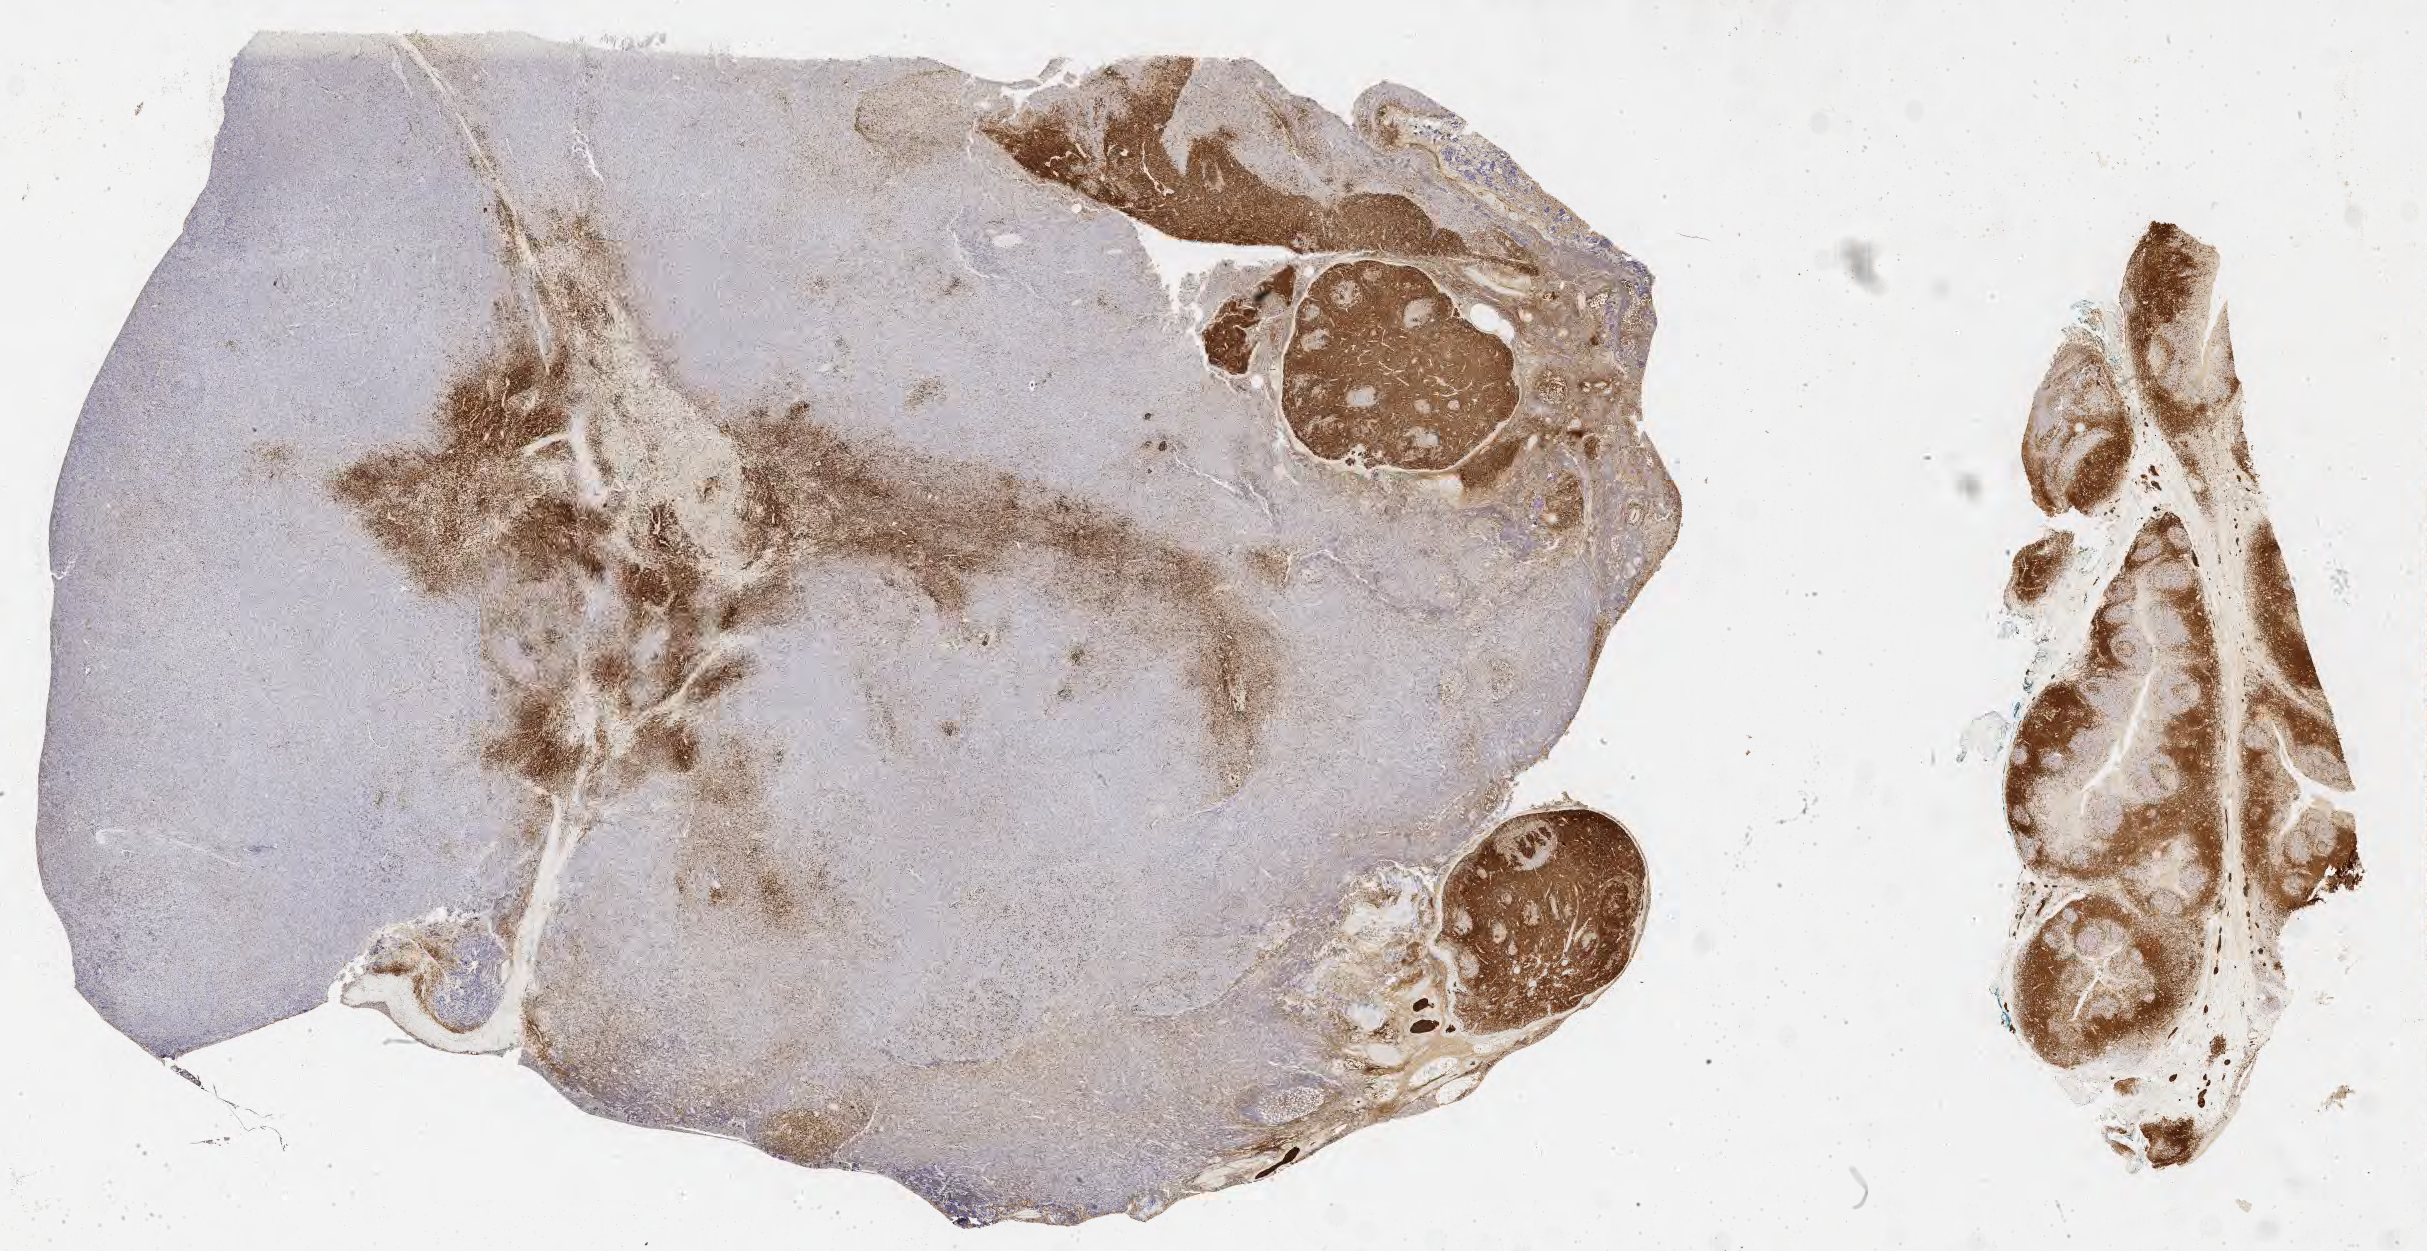
Whole-slide image, immunohistochemical stain for CD3 — low-resolution overview of the scanned area, about 39.2 x 20.2 mm, specimen: tumor tissue, site: lymph node of head and neck. Male, age 3 years at initial diagnosis.
- diagnosis: Burkitt lymphoma, NOS